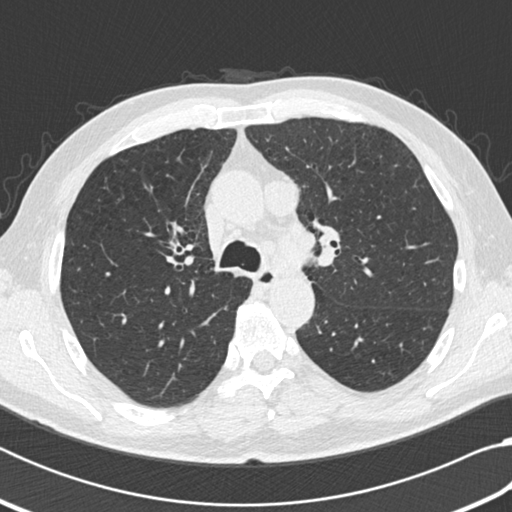
Chest CT (low-dose screening protocol), one axial image, third screening round (two years after baseline), lung window (W 1500 / L -600 HU), standard (soft-tissue) reconstruction kernel (B30f), slice 67 of 207 in the series. Male participant, aged 64 years at enrolment. Current smoker at enrolment.
Lesion marked by an expert reader, bounding box [x1, y1, x2, y2] px = [252, 176, 293, 216]. Screening reader's record for this exam: no non-calcified nodule ≥4 mm recorded. Official screen result: negative screen, significant abnormalities not suspicious for lung cancer.